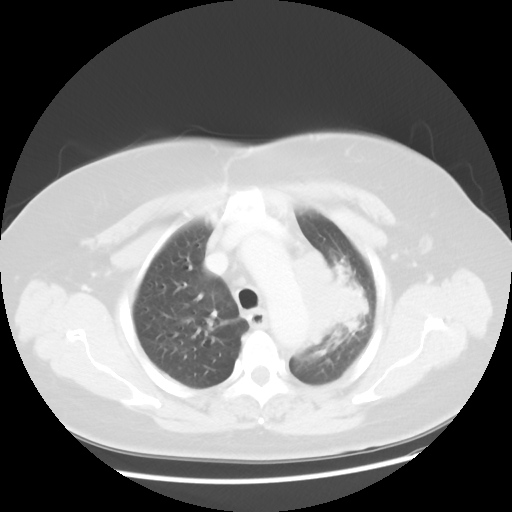
Chest CT, one axial slice; slice 37 of 49 in the series (ordered by position); lung window (W 1500 / L -600 HU); 5 mm slice thickness; 512 × 512 image matrix. Patient: female, 58 years. Case-level facts recorded for this patient, not image findings: clinical TNM (as recorded): T4 N3 M0.
Annotated regions visible in this slice (rectangle marked by the reading radiologist):
- lung tumour (recorded histology: small cell carcinoma): box from (x=294, y=245) to (x=384, y=362) px